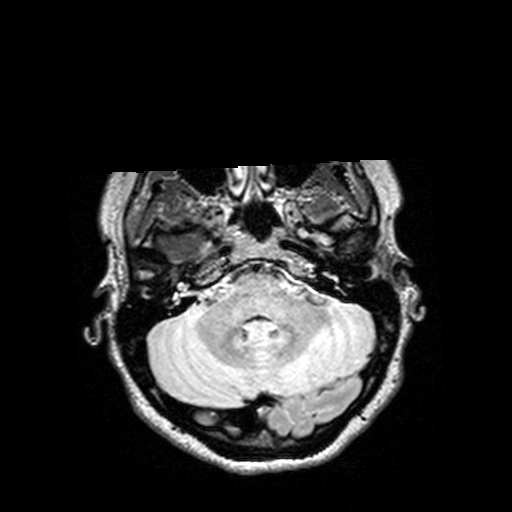
Brain MRI from a brain-tumour surgery series, one axial slice. Slice 111 of 144 in the series (ordered by position). T2 FLAIR. 512 × 512 image matrix, field of view 250 × 250 mm. From the clinical record (not read from this slice): histopathology: Astrocytoma; WHO grade: 3; IDH mutation: yes.
Outlined on this slice (outlined manually by an expert reader):
- tumour: box from (x=145, y=227) to (x=195, y=261) px